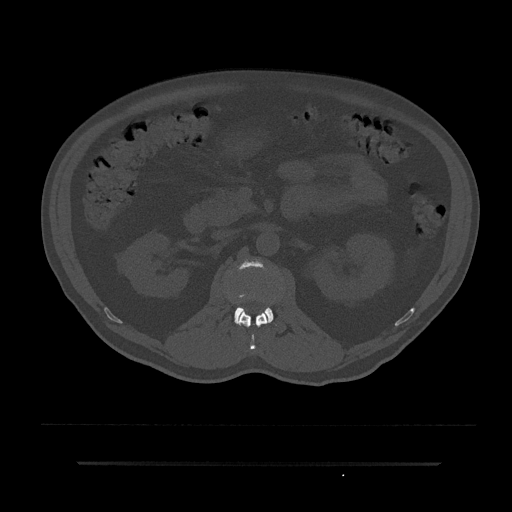
CT including the spine, one axial slice. Position 110 of 797 along the scan axis. Bone window (W 1800 / L 400 HU). 0.5 mm slice thickness. 512 × 512 image matrix. Patient: male, 59 years. From the clinical record (not read from this slice): primary cancer: bile ducts; vertebrae with lytic lesions (as recorded): T10.
Structures marked on this image (semi-automatically segmented with operator editing):
- L1 vertebra: bounding box (x1, y1, x2, y2) in pixels: (238, 311, 267, 350)
- L2 vertebra: (234, 261, 273, 324)